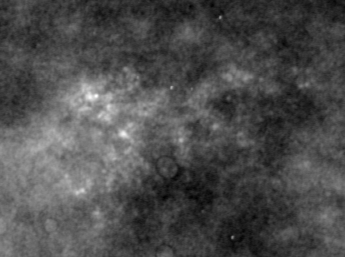
Region of interest cut from a scanned film mammogram (one marked finding), left breast, CC view.
- Calcifications, morphology pleomorphic, distribution clustered; BI-RADS assessment category 4; pathology result (as recorded, not read from the image): malignant.